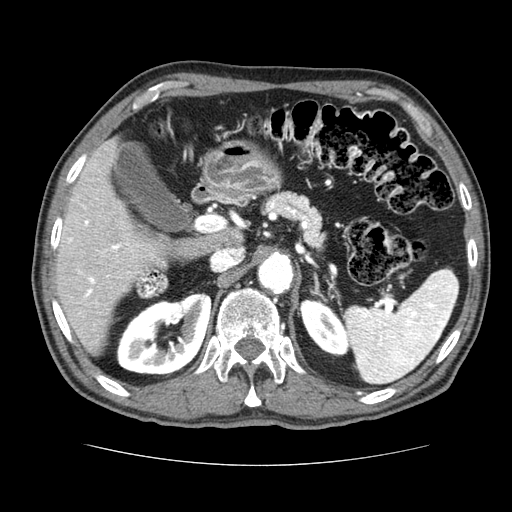
Contrast-enhanced abdominal CT (liver protocol), one axial slice; position 42 of 79 along the scan axis; reconstruction kernel STANDARD; soft-tissue window (W 400 / L 40 HU); 512 × 512 image matrix, field of view 360 × 360 mm. From the clinical record (not read from this slice): diagnosis: hepatocellular carcinoma (patient treated with transarterial chemoembolisation; whether this scan precedes or follows treatment is not stated here); TNM stage (as recorded): Stage-I; Child-Pugh class: A.
Annotated regions visible in this slice (semi-automatically segmented with operator editing):
- liver parenchyma outside the tumour (the mass and vessels are separate outlines, so this box may not span the whole liver): bounding box [x1, y1, x2, y2] px = [54, 138, 166, 354]
- liver vessels: [66, 205, 133, 314]